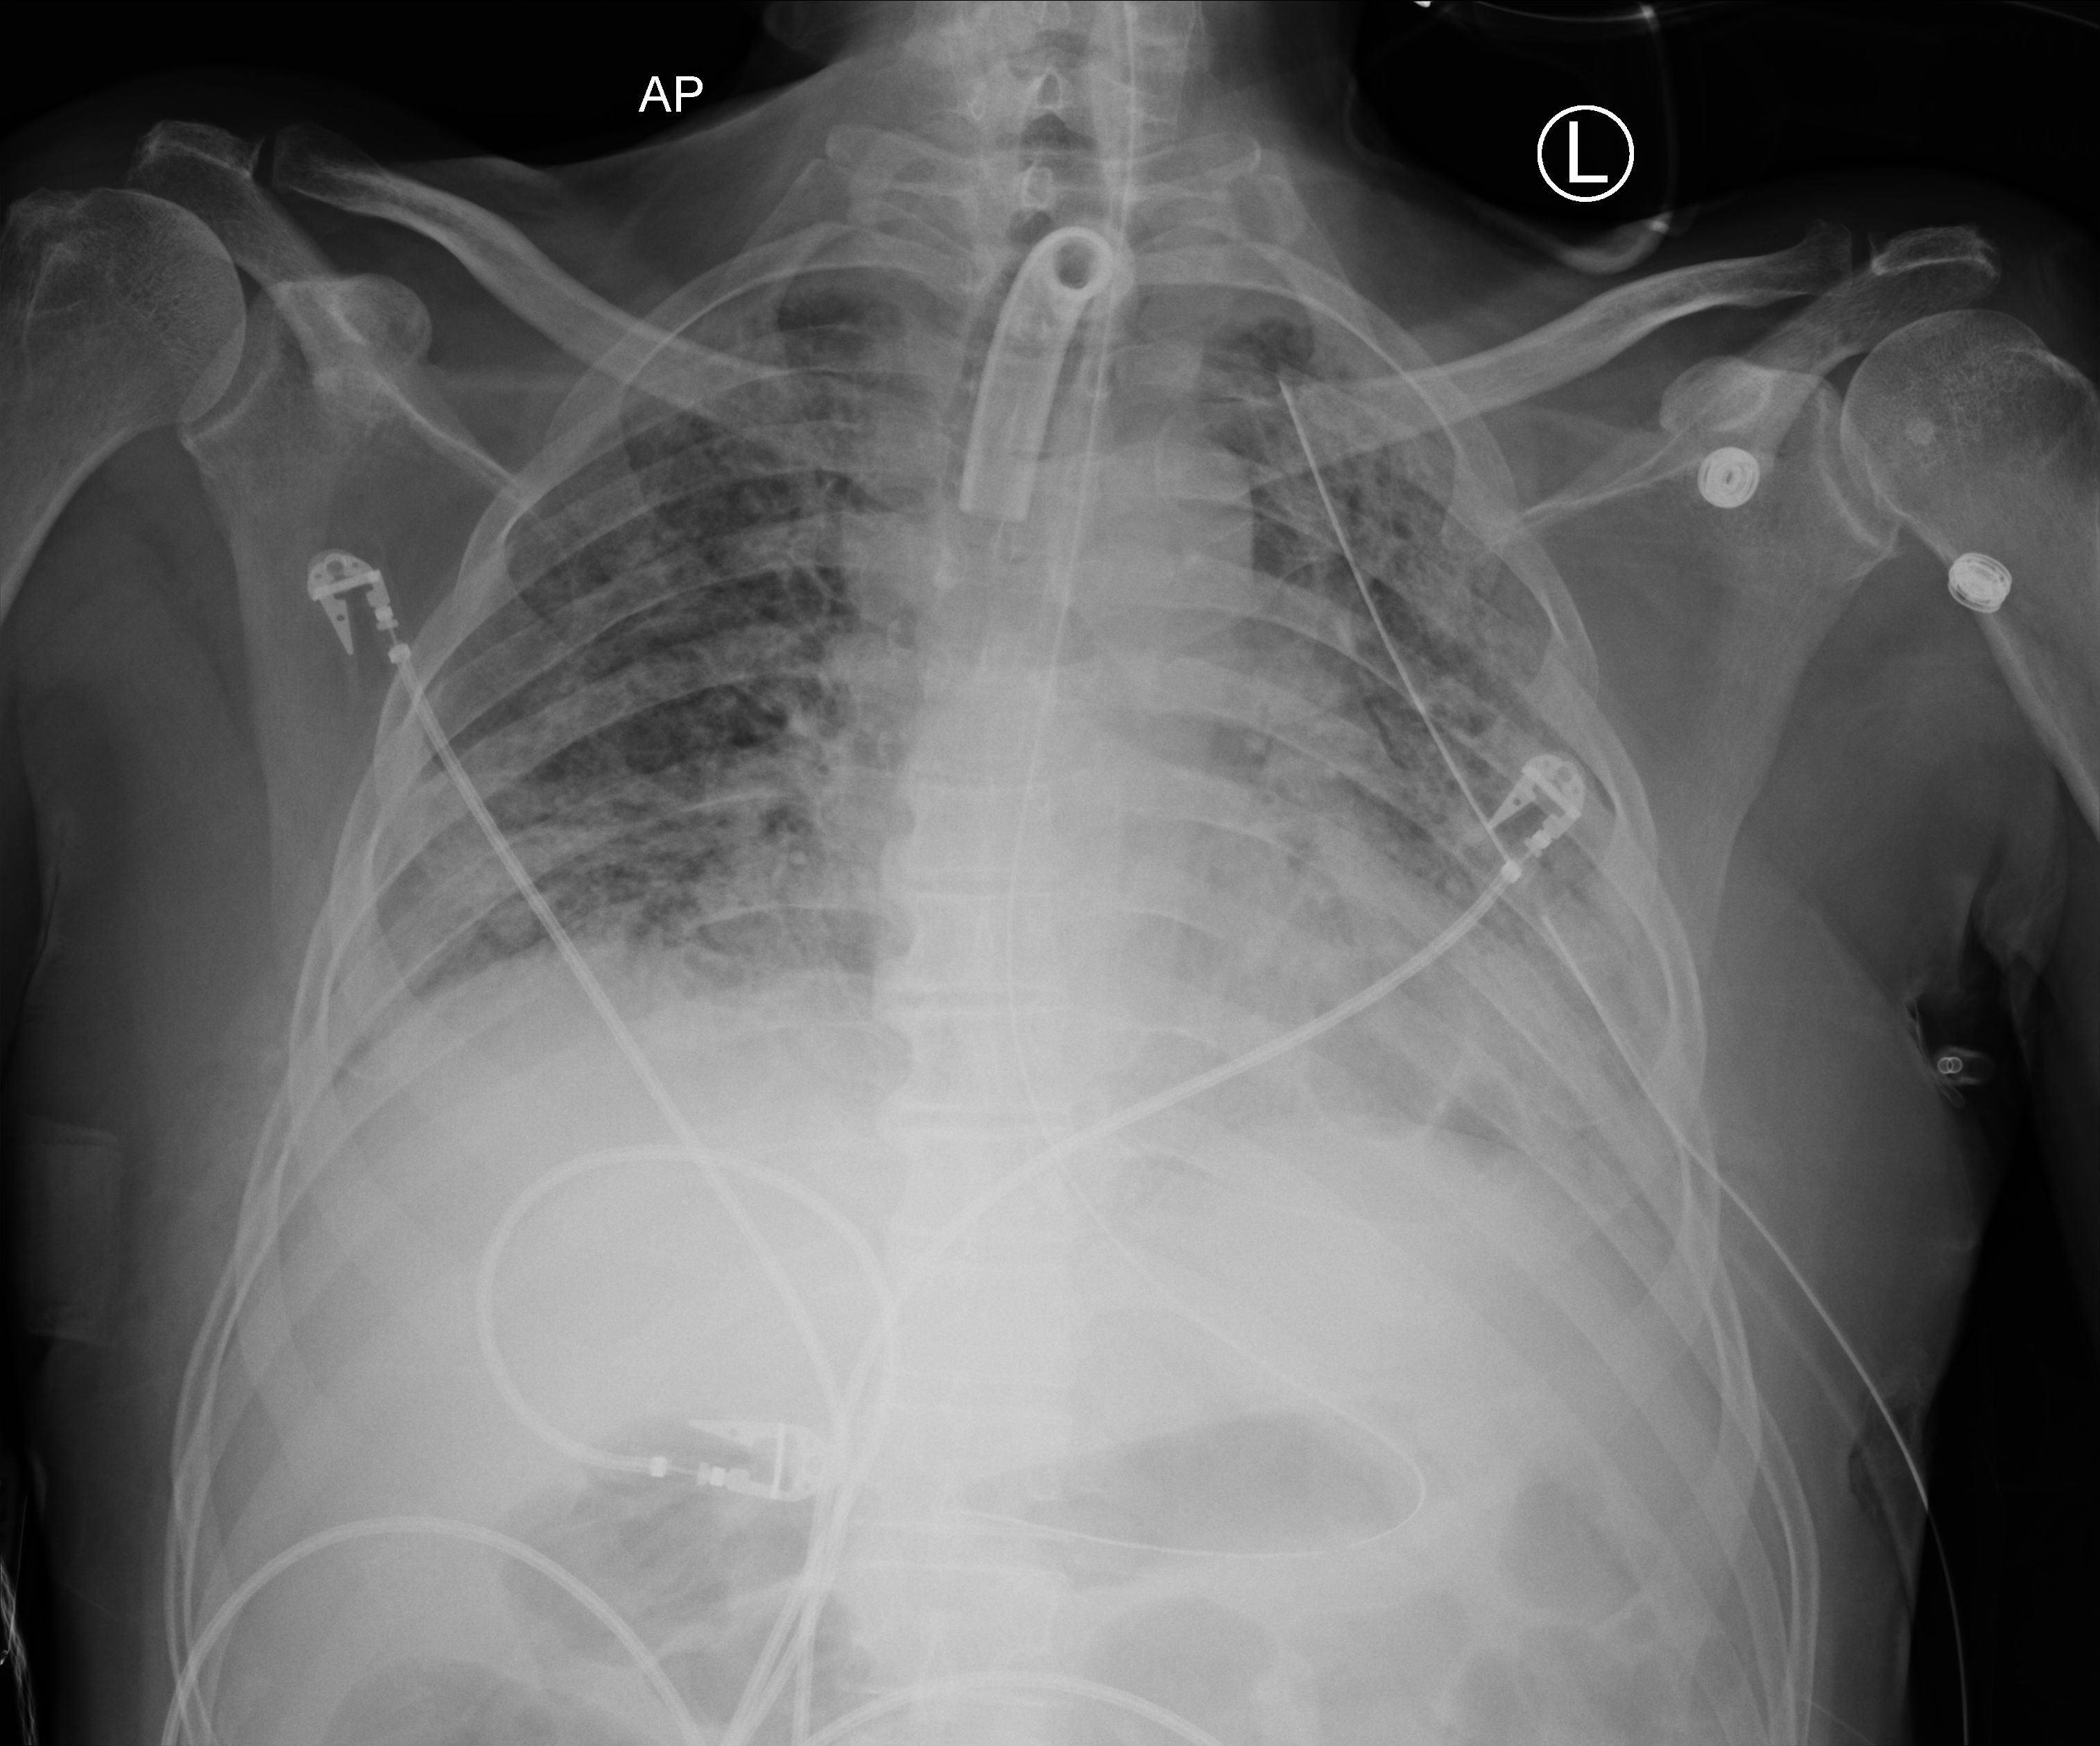
Bedside chest radiograph (computed radiography), anteroposterior (AP) projection. Patient hospitalised with COVID-19; male, aged 18–59 years.
From the hospital-stay record, not from the radiograph (when in the stay this image was taken is not recorded): mechanically ventilated during this hospital stay: yes; admitted to intensive care during this hospital stay: yes; diabetes (admission record): no.